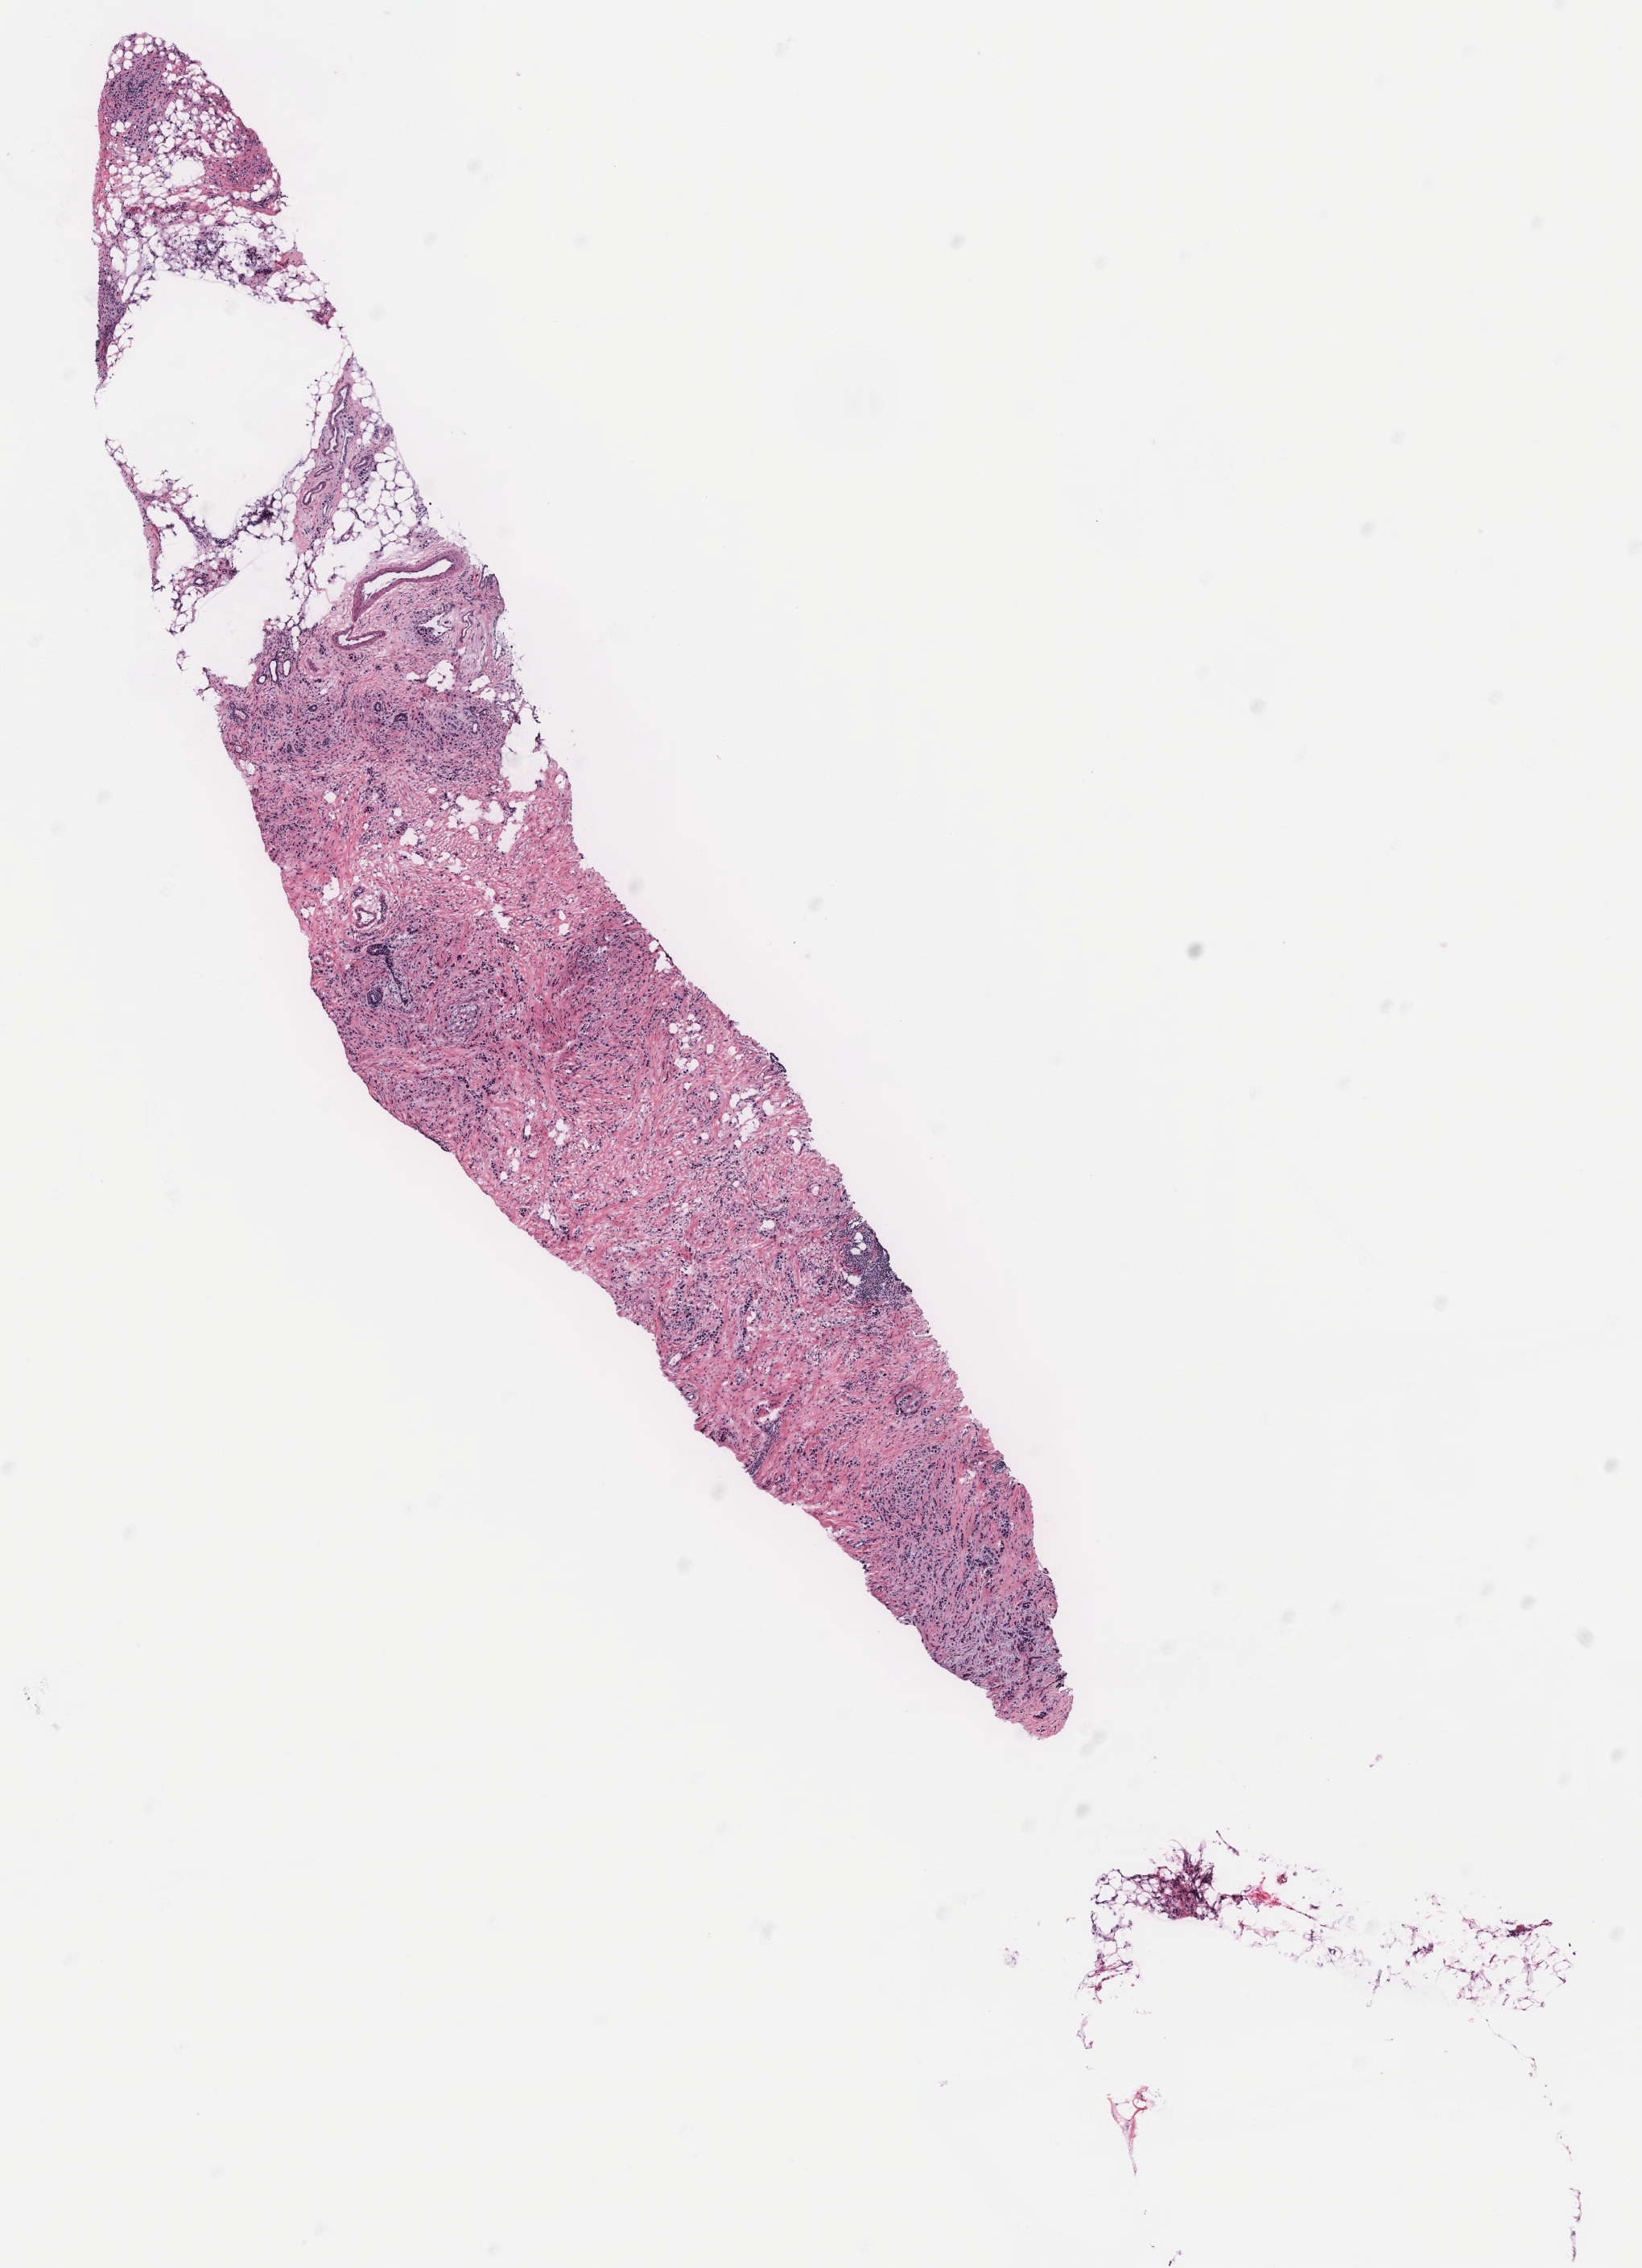
Digitized H&E tissue section (whole slide), shown as a low-resolution overview of the whole scanned area (about 8.2 x 11.3 mm, acquisition: 40x scan); breast, tumour tissue. Female, 51 y/o.
• diagnosis: Infiltrating duct carcinoma, NOS